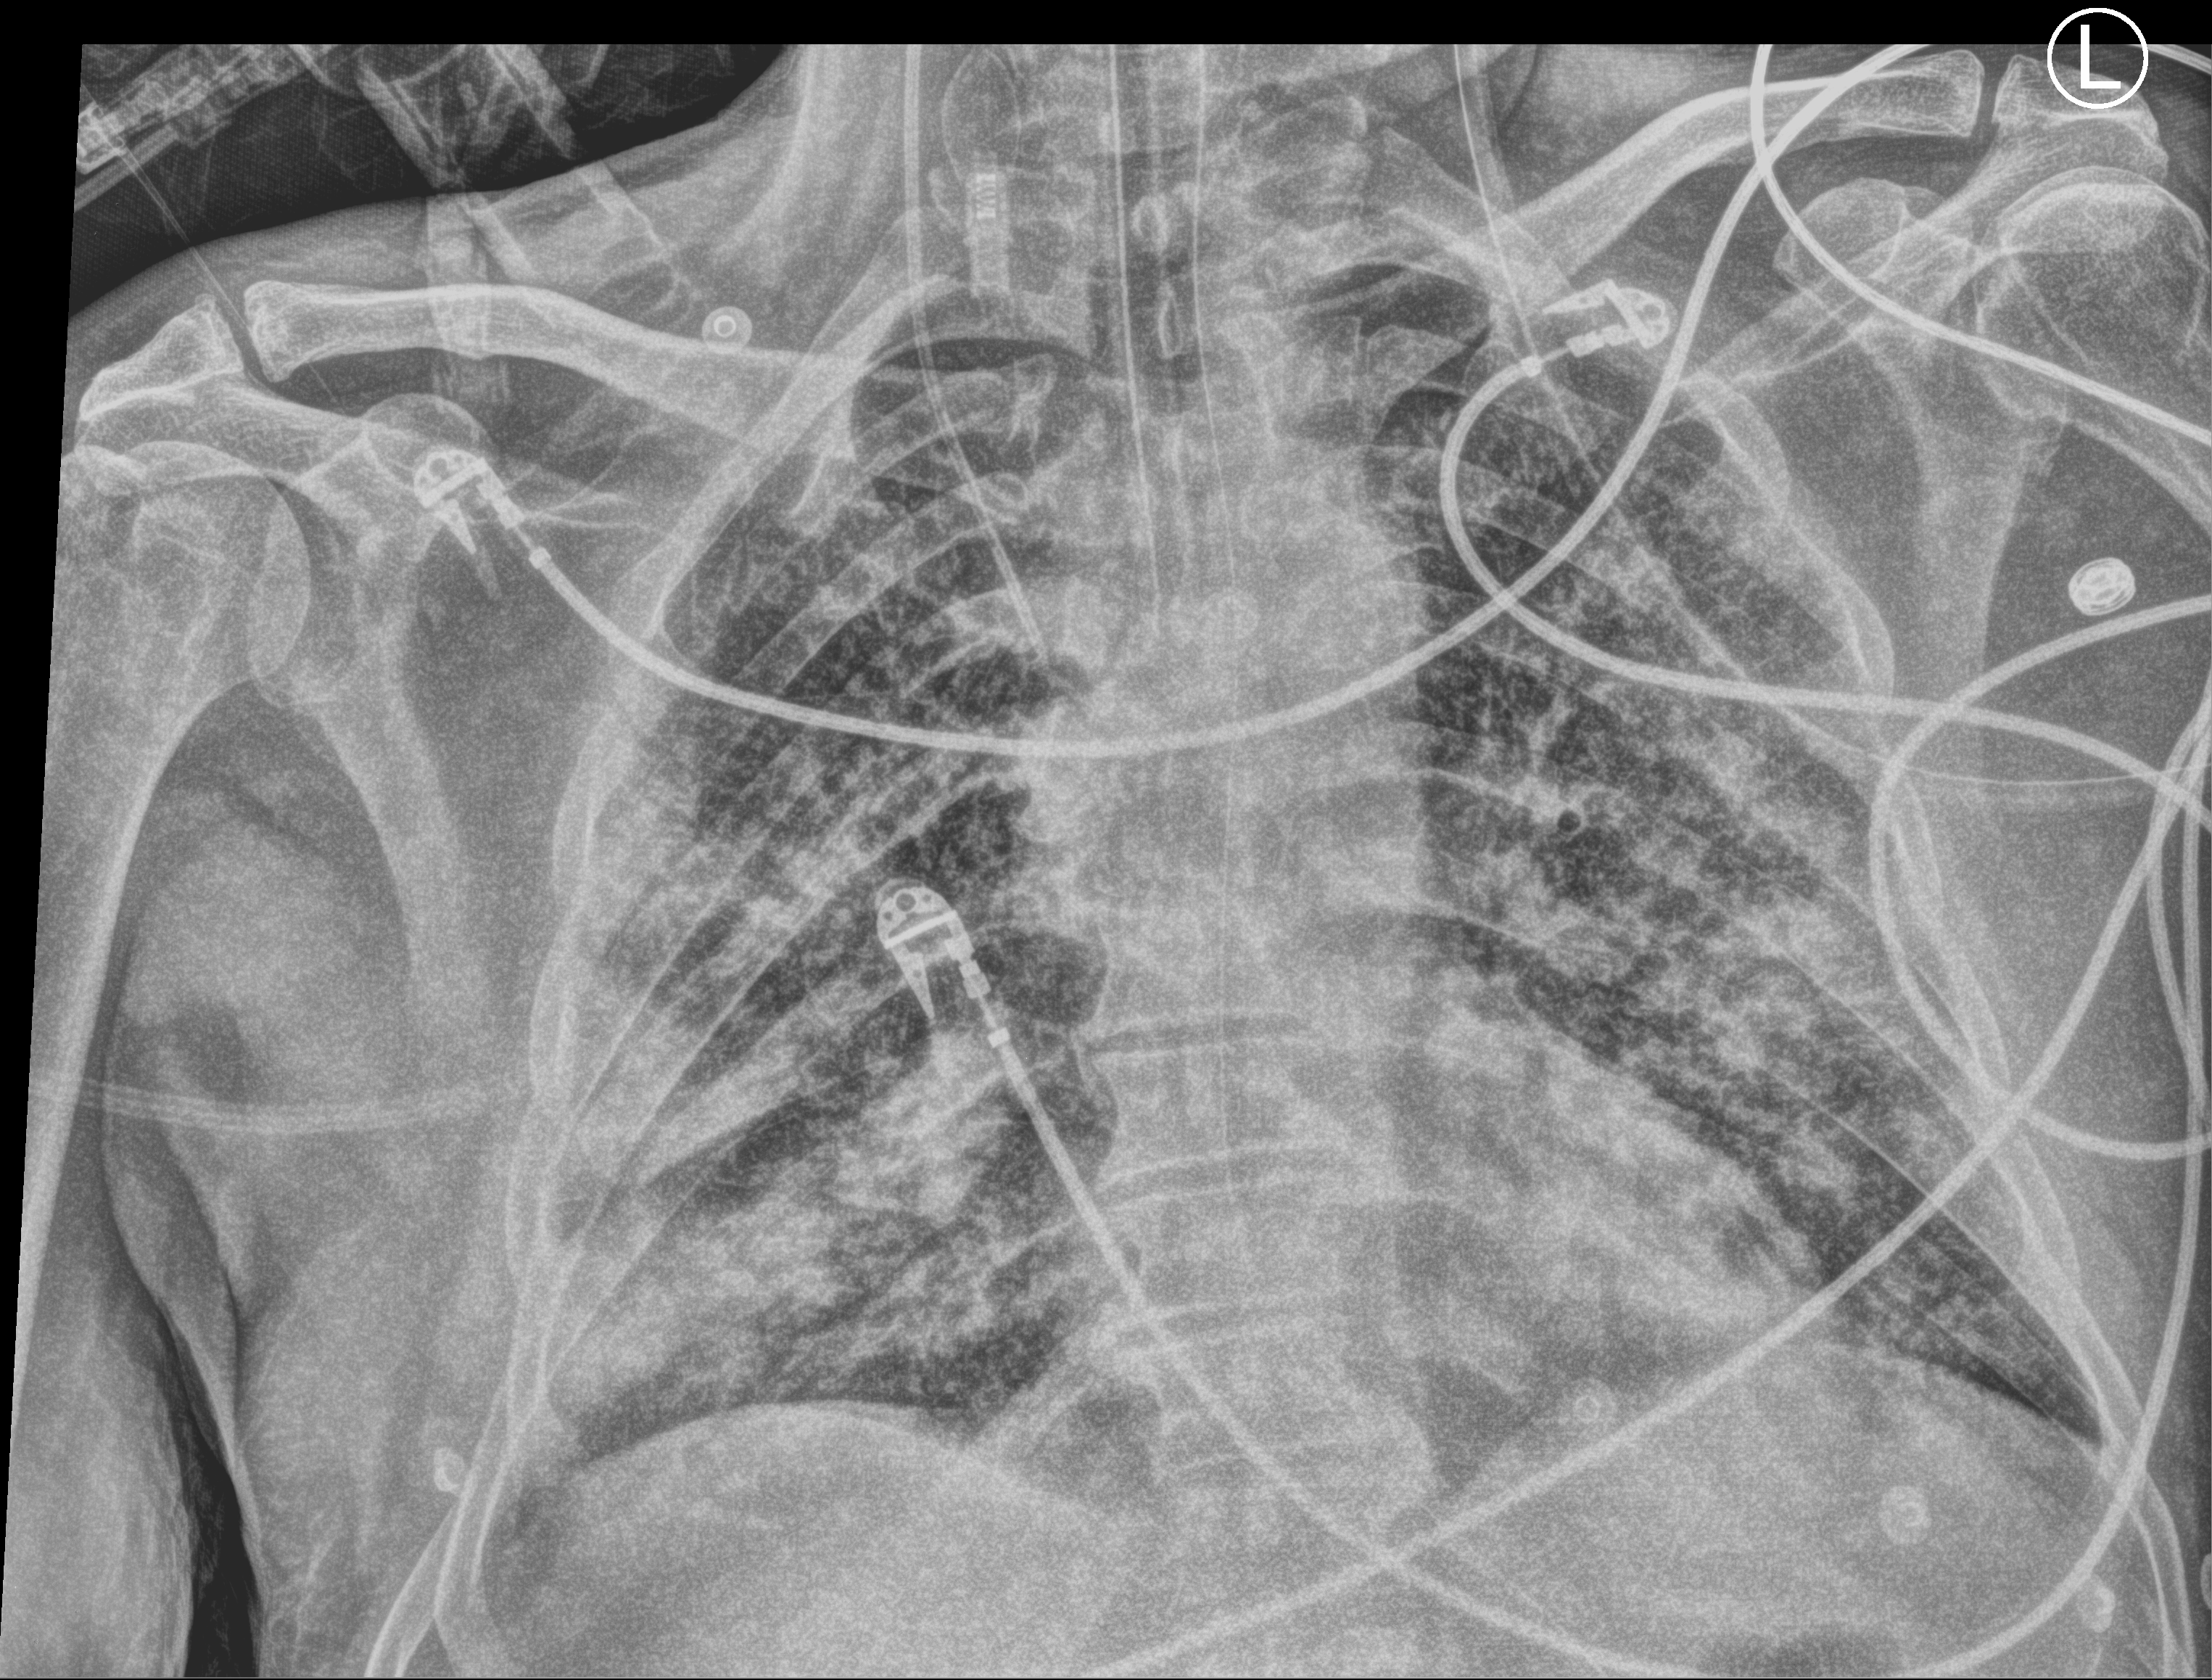
Chest X-ray (portable), anteroposterior (AP) projection. Male patient hospitalised with COVID-19, age 60–74 years.
Admission-level facts for this patient (not findings on this image; timing relative to this image not recorded):
- mechanically ventilated during this hospital stay: yes
- hypertension (admission record): yes
- admitted to intensive care during this hospital stay: yes